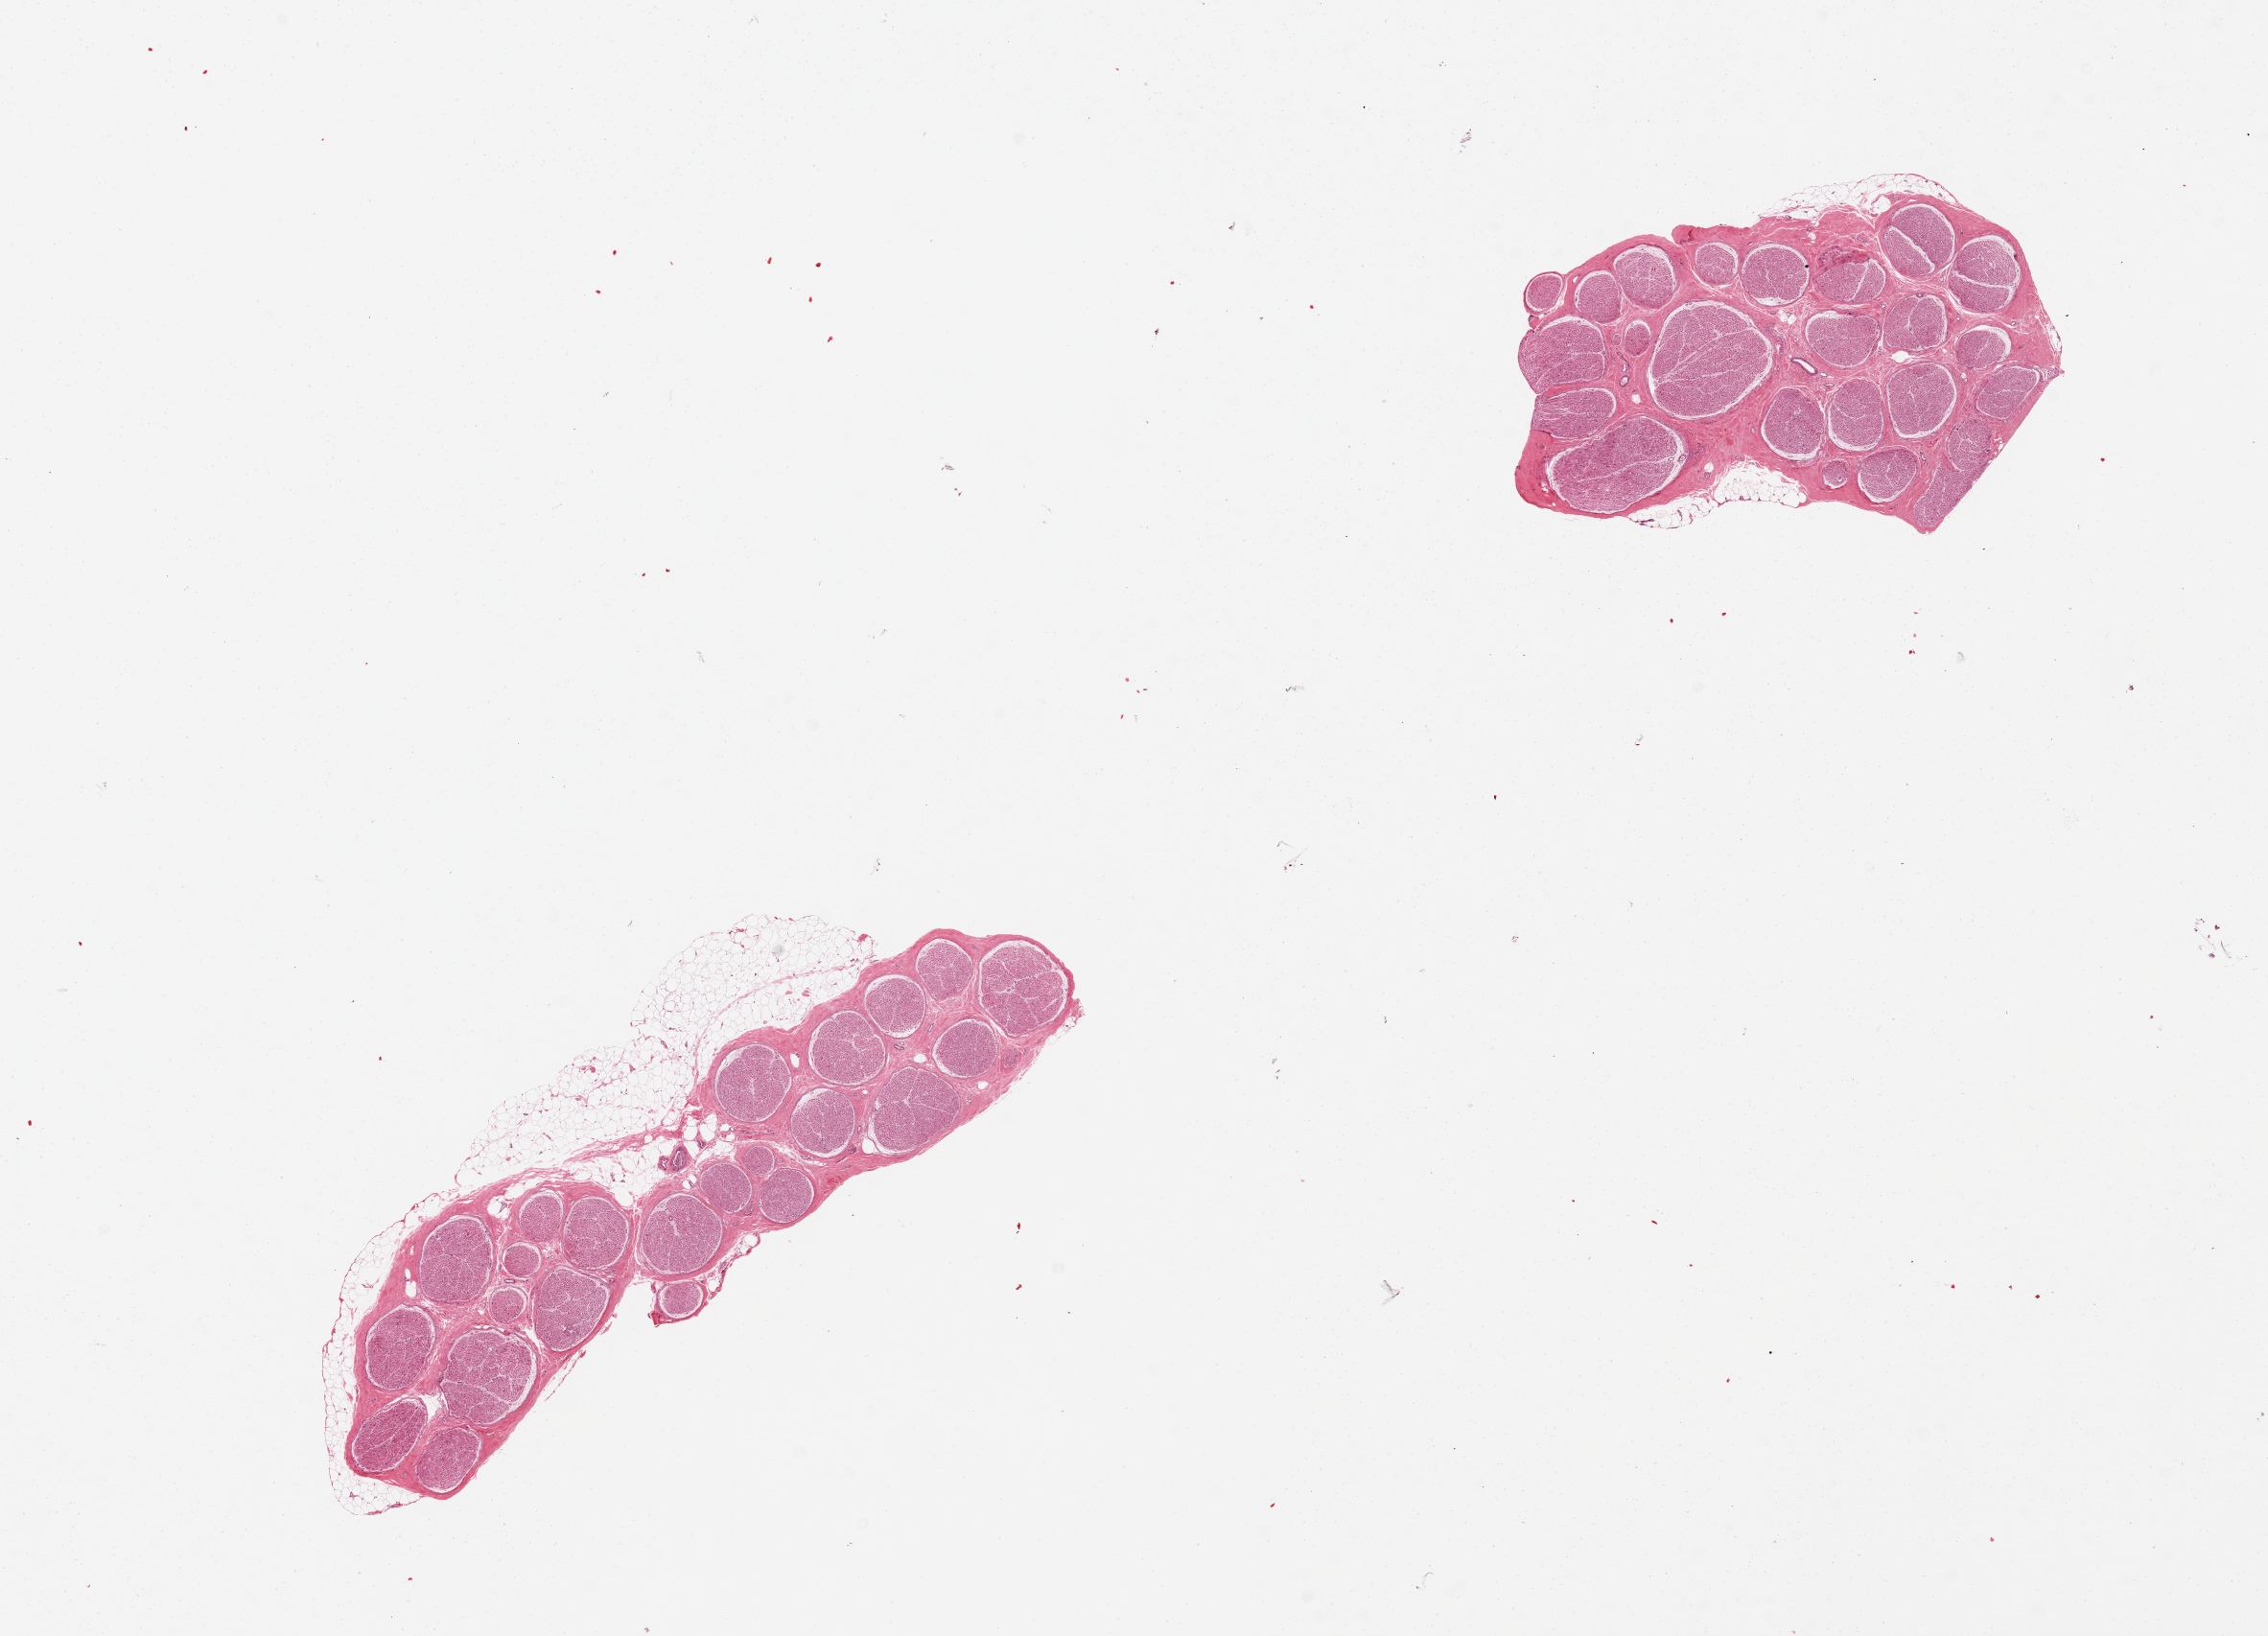
Whole-slide image, H&E stain — whole scanned area (about 18.7 x 13.5 mm) shown as a low-resolution overview, PAXgene-fixed paraffin-embedded (PFPE) section, section of tibial nerve (target tissue), tissue donor sample. Female donor.
Pathologist's review note for this sample: 2 pieces, nubbin of adherent fat up to 0.6mm on one aliquot.